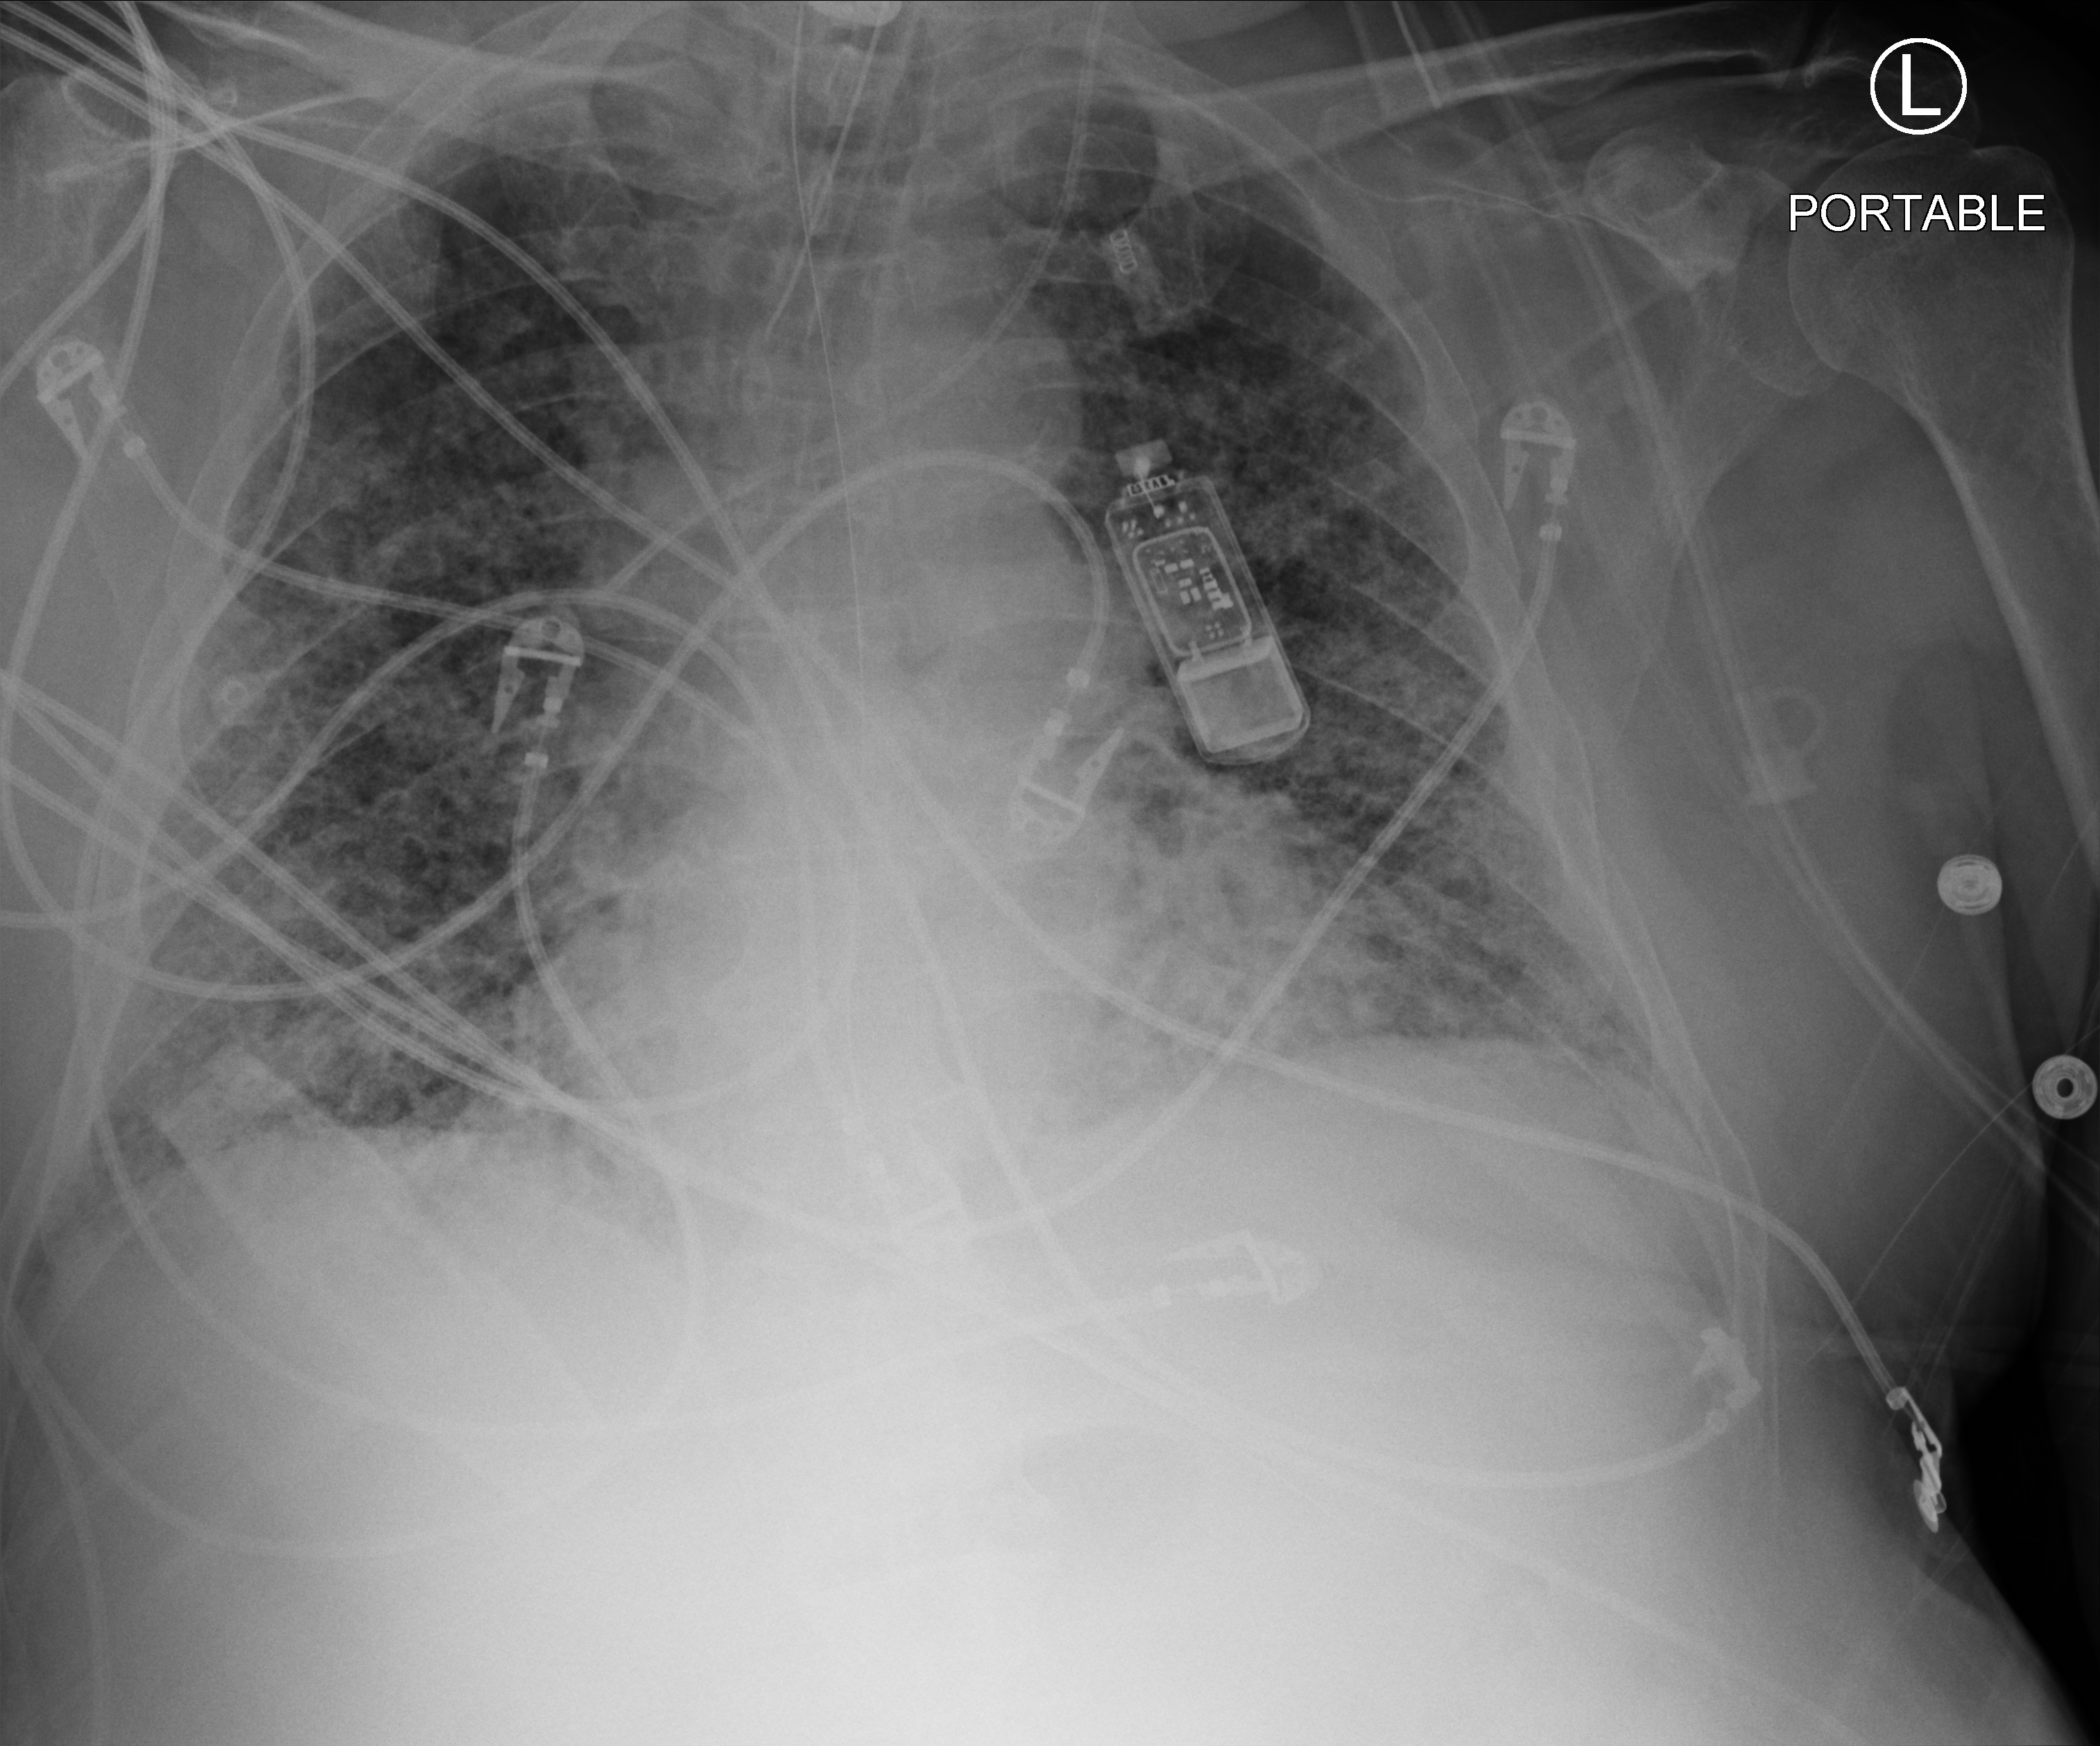
Bedside chest radiograph (computed radiography), anteroposterior (AP) projection. Patient hospitalised with COVID-19; male, aged 60–74 years.
From the hospital-stay record, not from the radiograph (when in the stay this image was taken is not recorded):
- length of hospital stay: 7 days
- admitted to intensive care during this hospital stay: yes